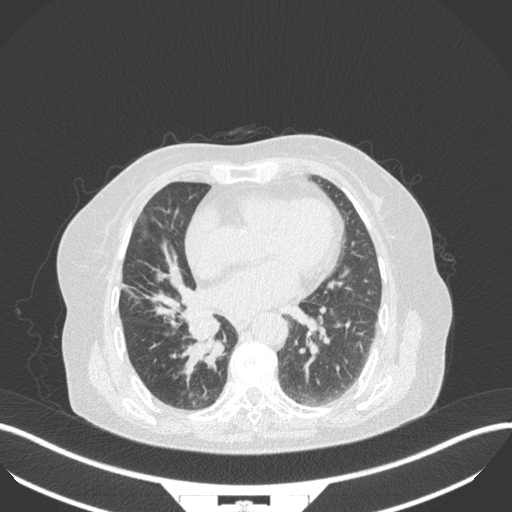
Chest CT, one axial slice; slice 134 of 329 in the series (ordered by position); 120 kVp; lung window (W 1500 / L -600 HU); 1 mm slice thickness; 512 × 512 image matrix, field of view 400 × 400 mm. Female patient, age 75 years. From the clinical record (not read from this slice): clinical TNM (as recorded): T1b N0 M1a; histopathological grade: G1.
Structures marked on this image (bounding box drawn by a radiologist):
- lung tumour (recorded histology: squamous cell carcinoma): bounding box <174,309,225,380> (left, top, right, bottom; pixels)